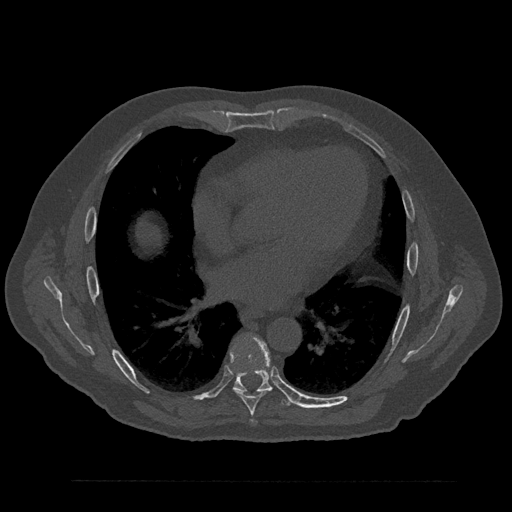
CT including the spine, one axial slice; 120 kVp; bone window (W 1800 / L 400 HU); 512 × 512 image matrix, field of view 430 × 430 mm. Patient: male, 61 years. Case-level facts recorded for this patient, not image findings: primary cancer: prostate.
Structures marked on this image (semi-automatically segmented with operator editing):
- T7 vertebra: box from (x=231, y=346) to (x=265, y=422) px
- T8 vertebra: (x=233, y=336)–(x=293, y=406)